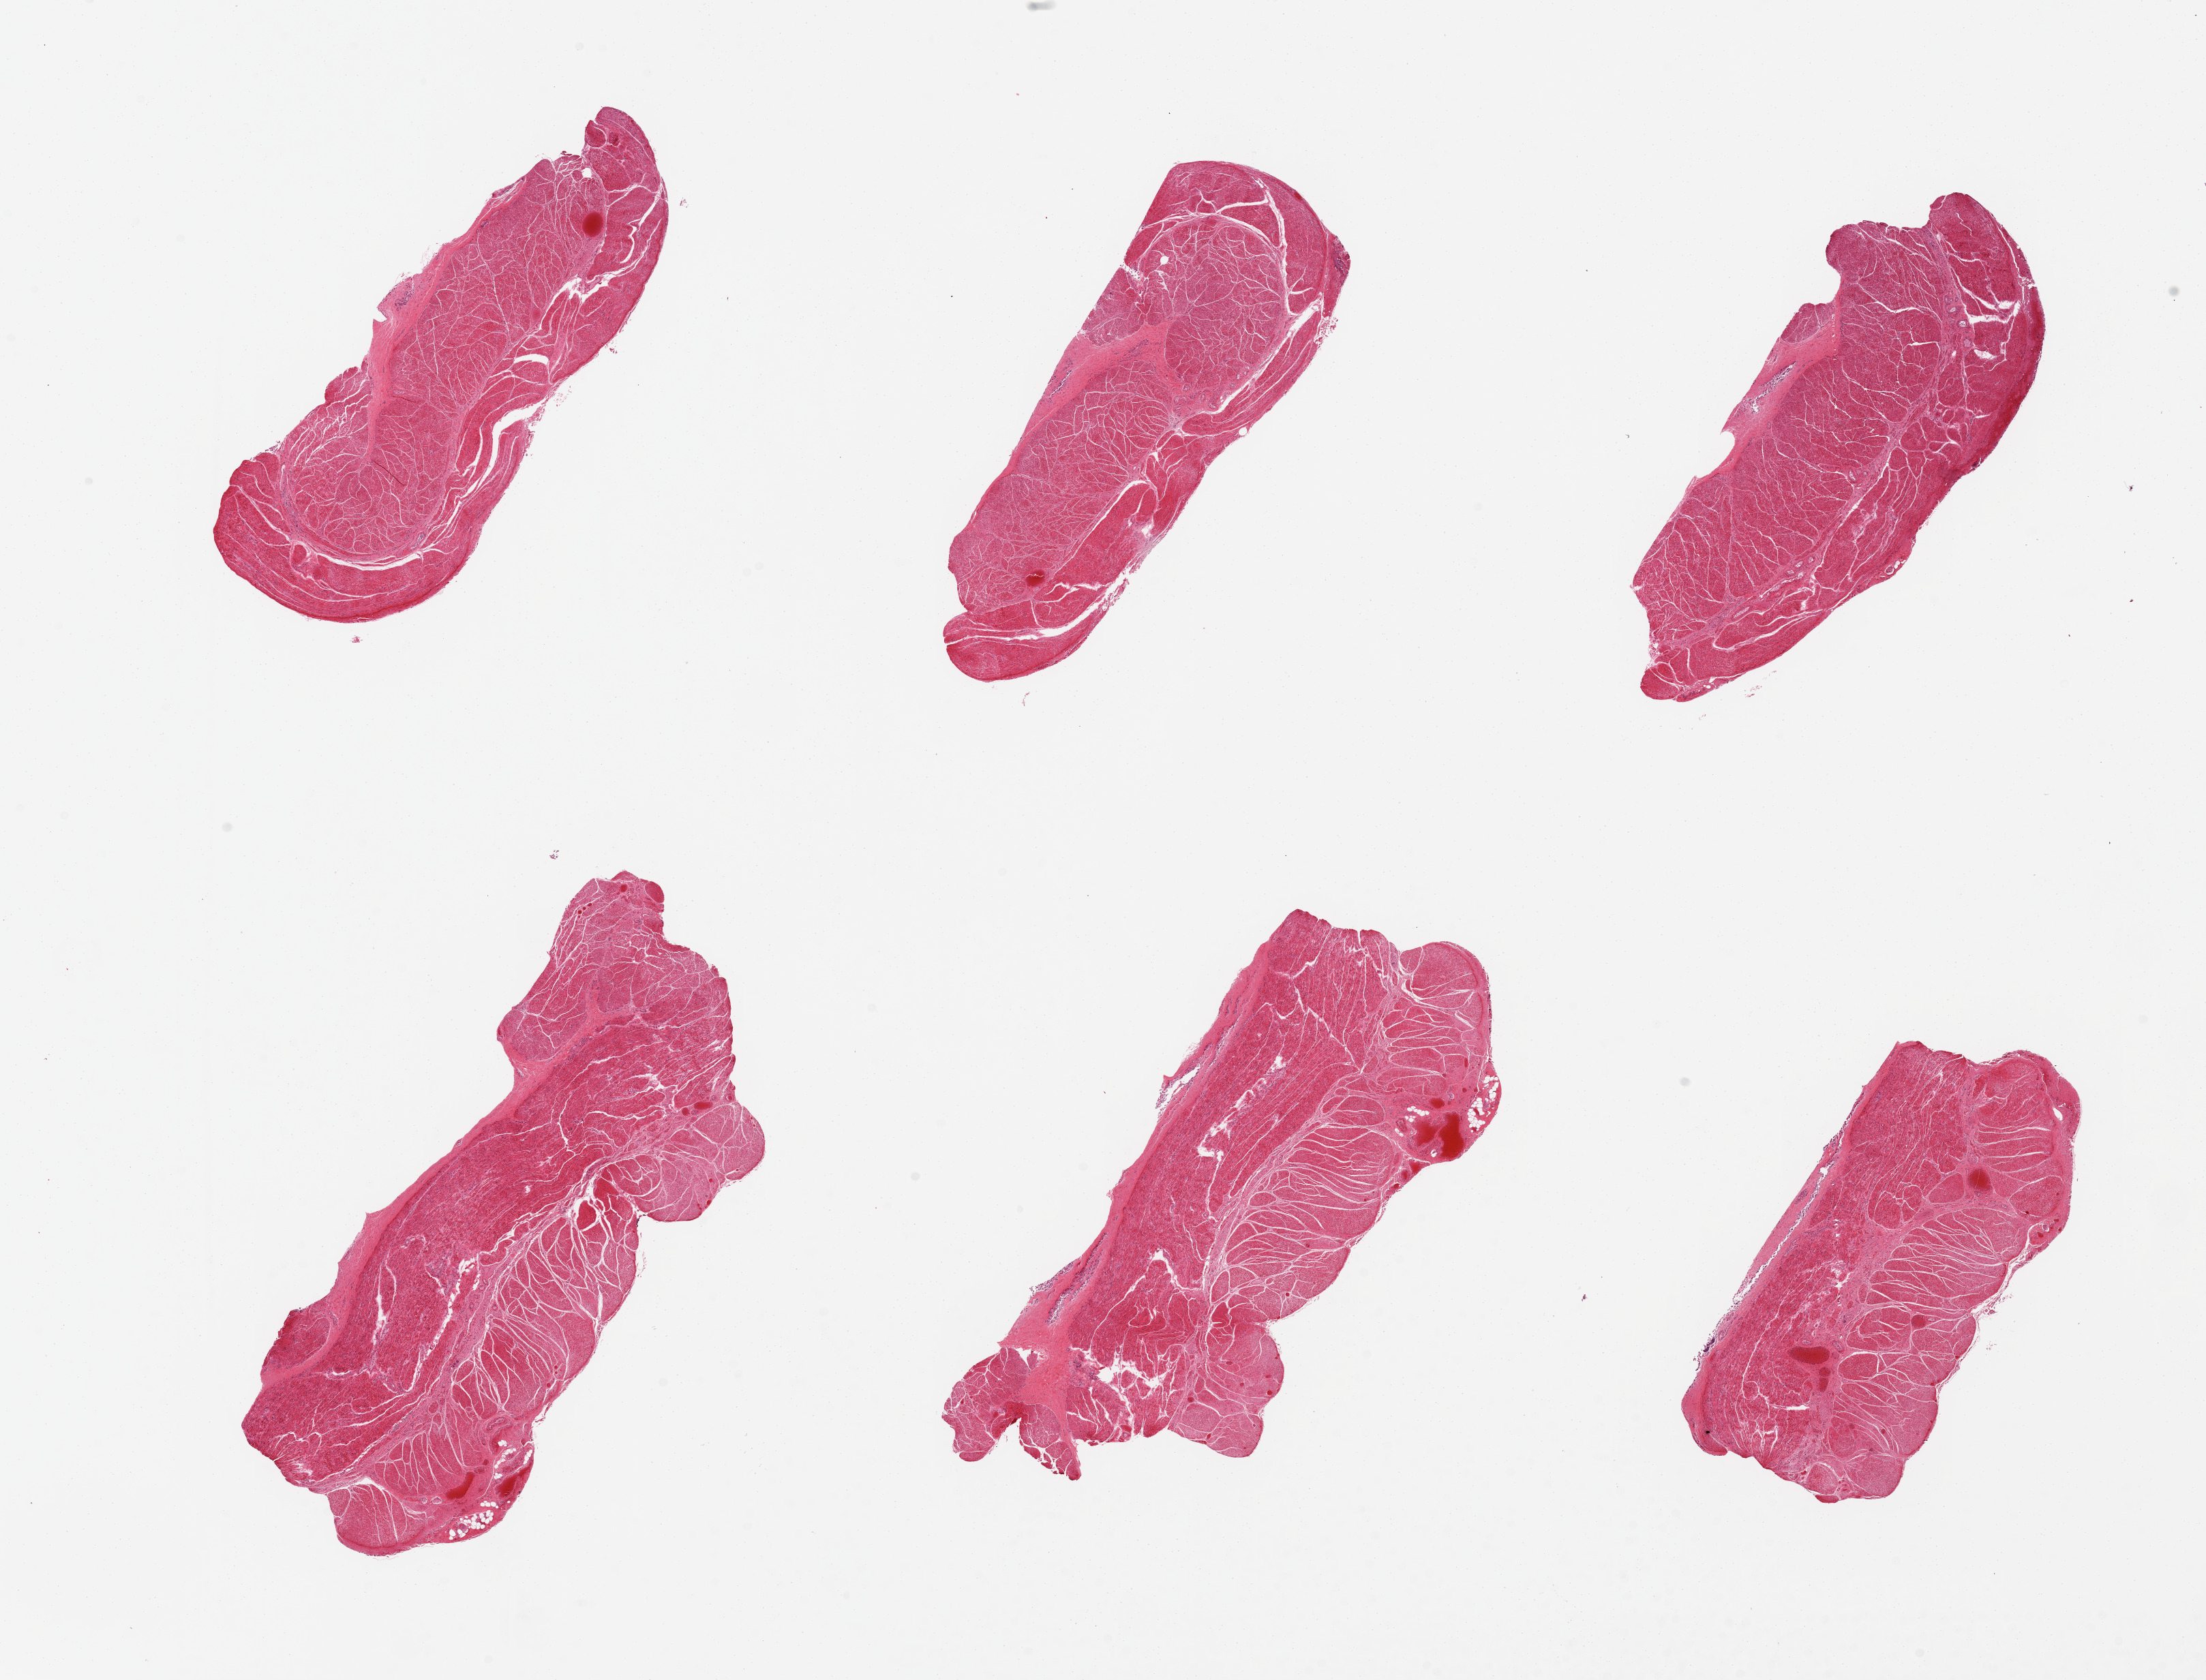
Digitized H&E-stained section — shown as a low-resolution overview of the whole scanned area (about 25.6 x 19.5 mm, from a 20x scan); PAXgene-fixed paraffin-embedded (PFPE) section; section of esophageal muscle (target tissue); donor tissue sample. Donor sex: male.
Review note (as recorded): 6 pieces, all muscularis, good specimens.